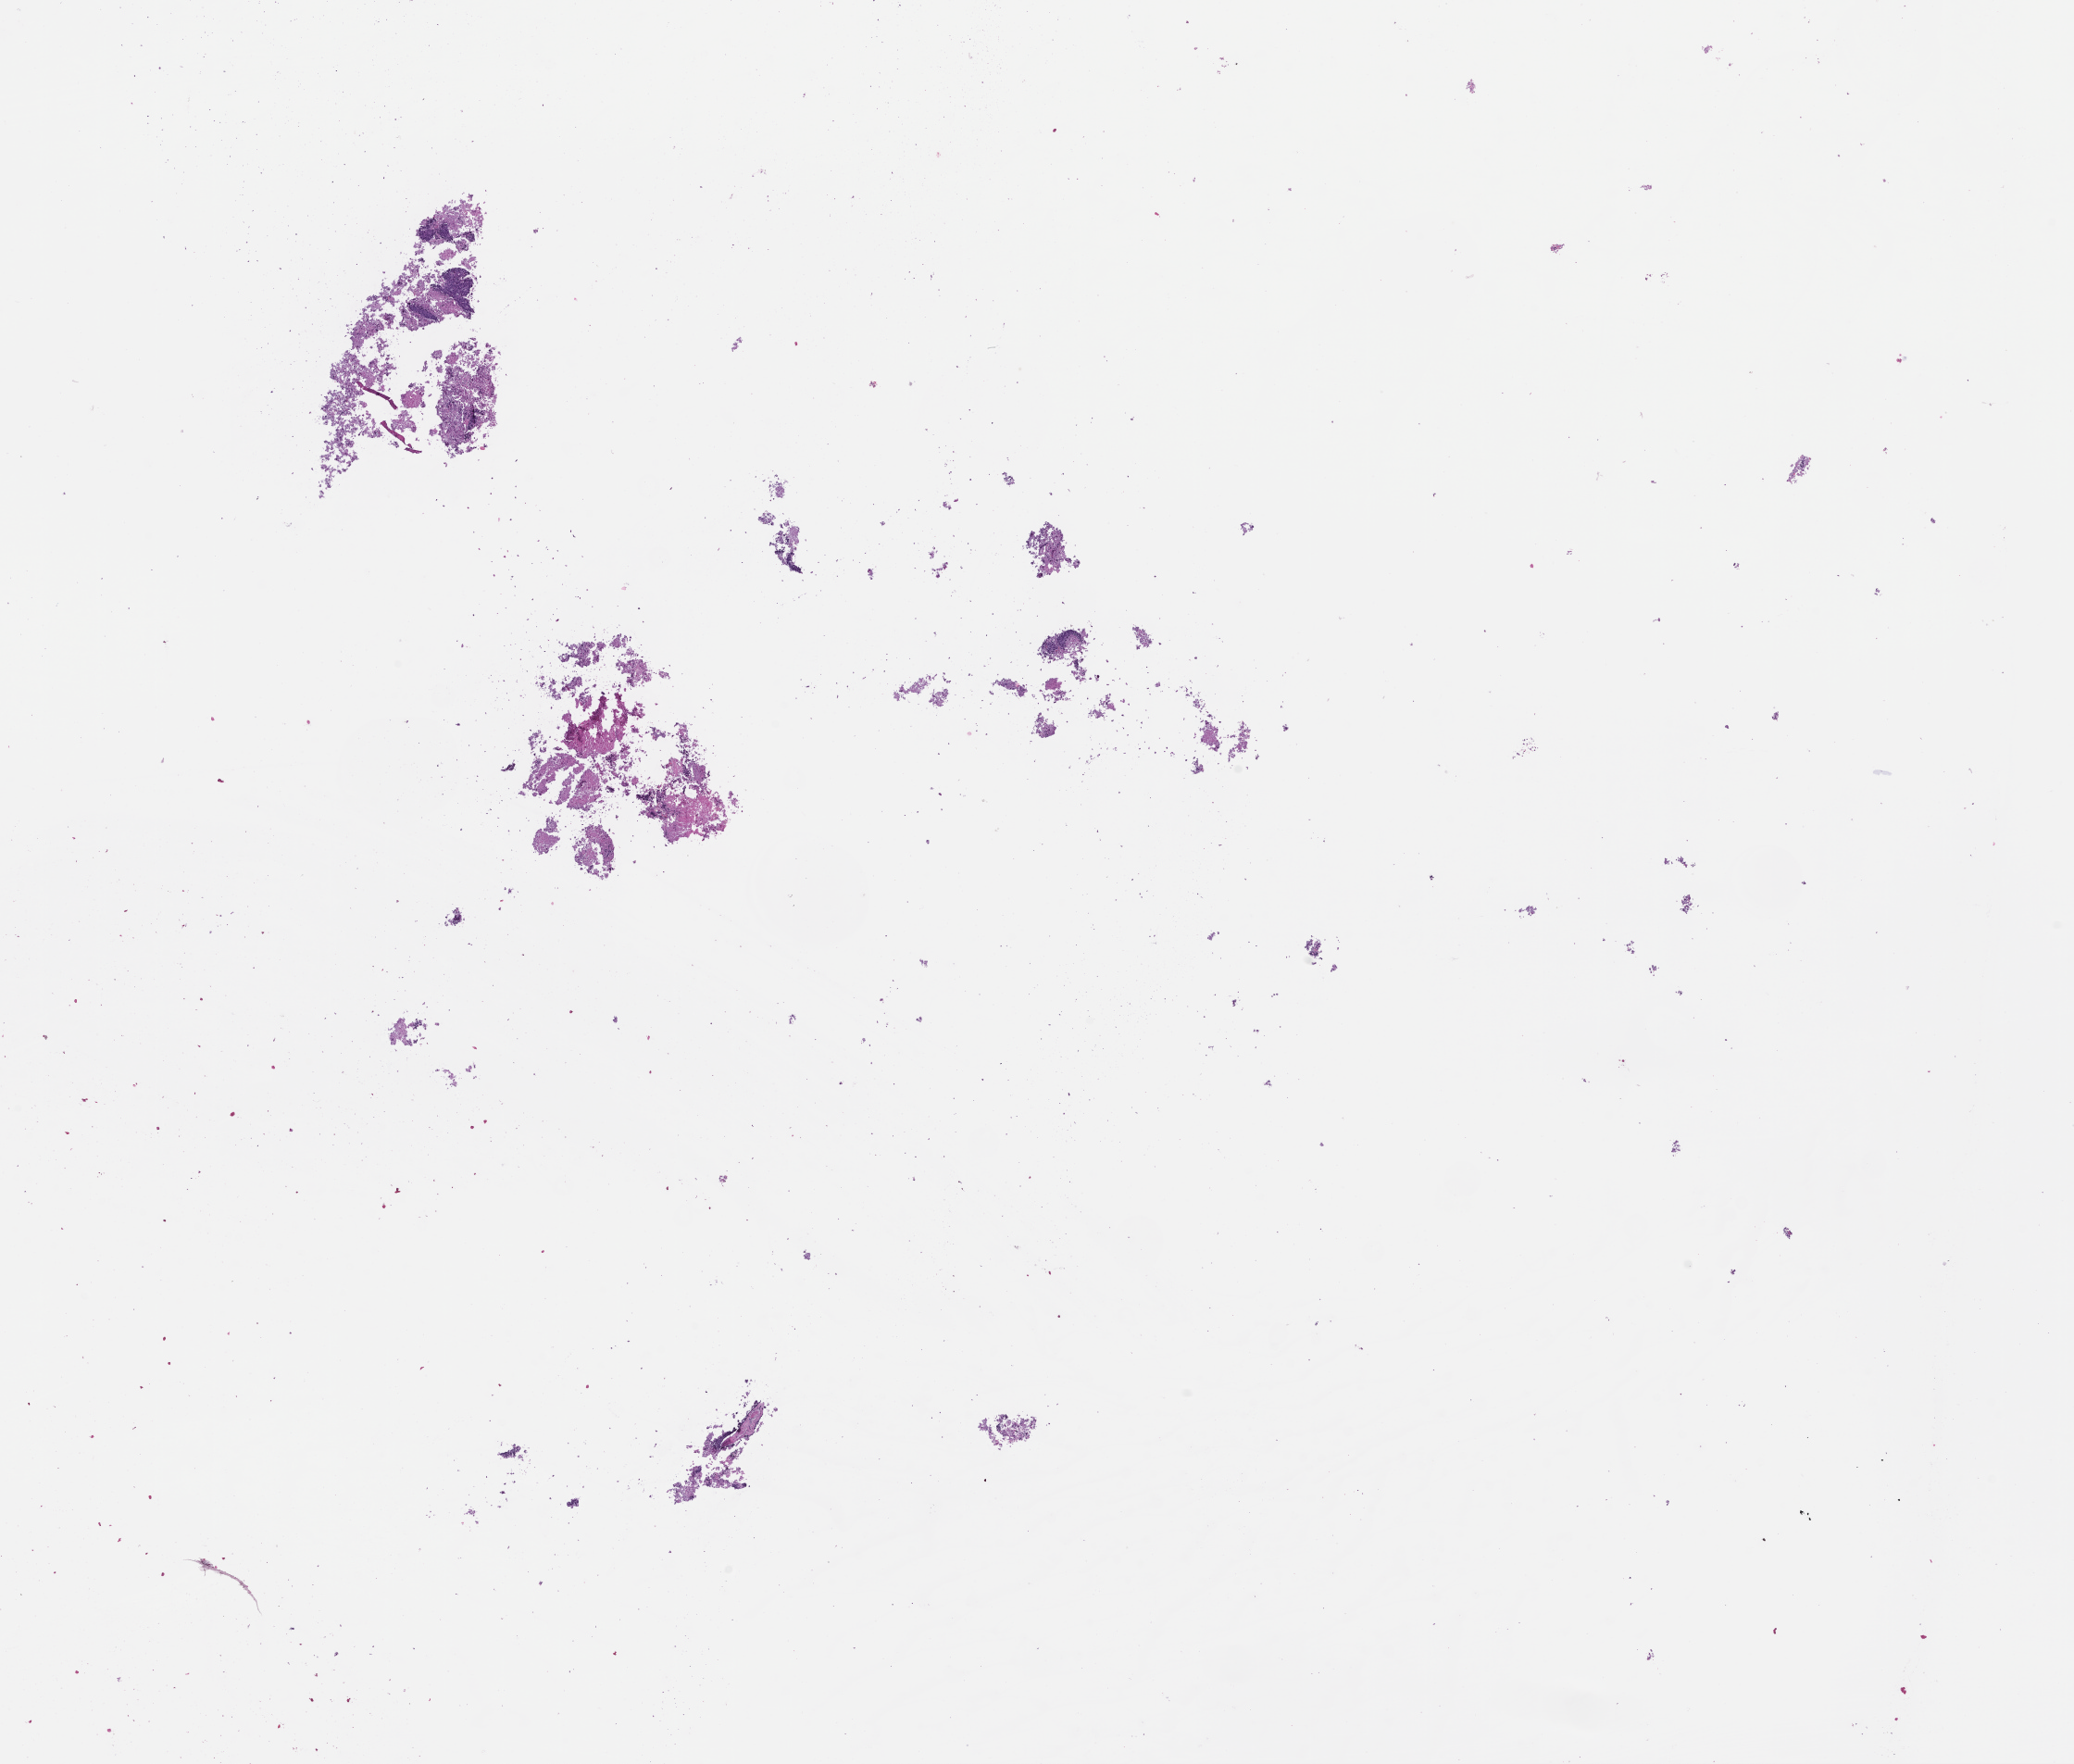
Haematoxylin and eosin whole-slide image — shown as a low-resolution overview of the whole scanned area (about 18.1 x 15.4 mm), formalin-fixed paraffin-embedded section, tissue site: lung. Male patient.
This section: primary tumour tissue. Diagnosis: Non-Small Cell Lung Carcinoma.